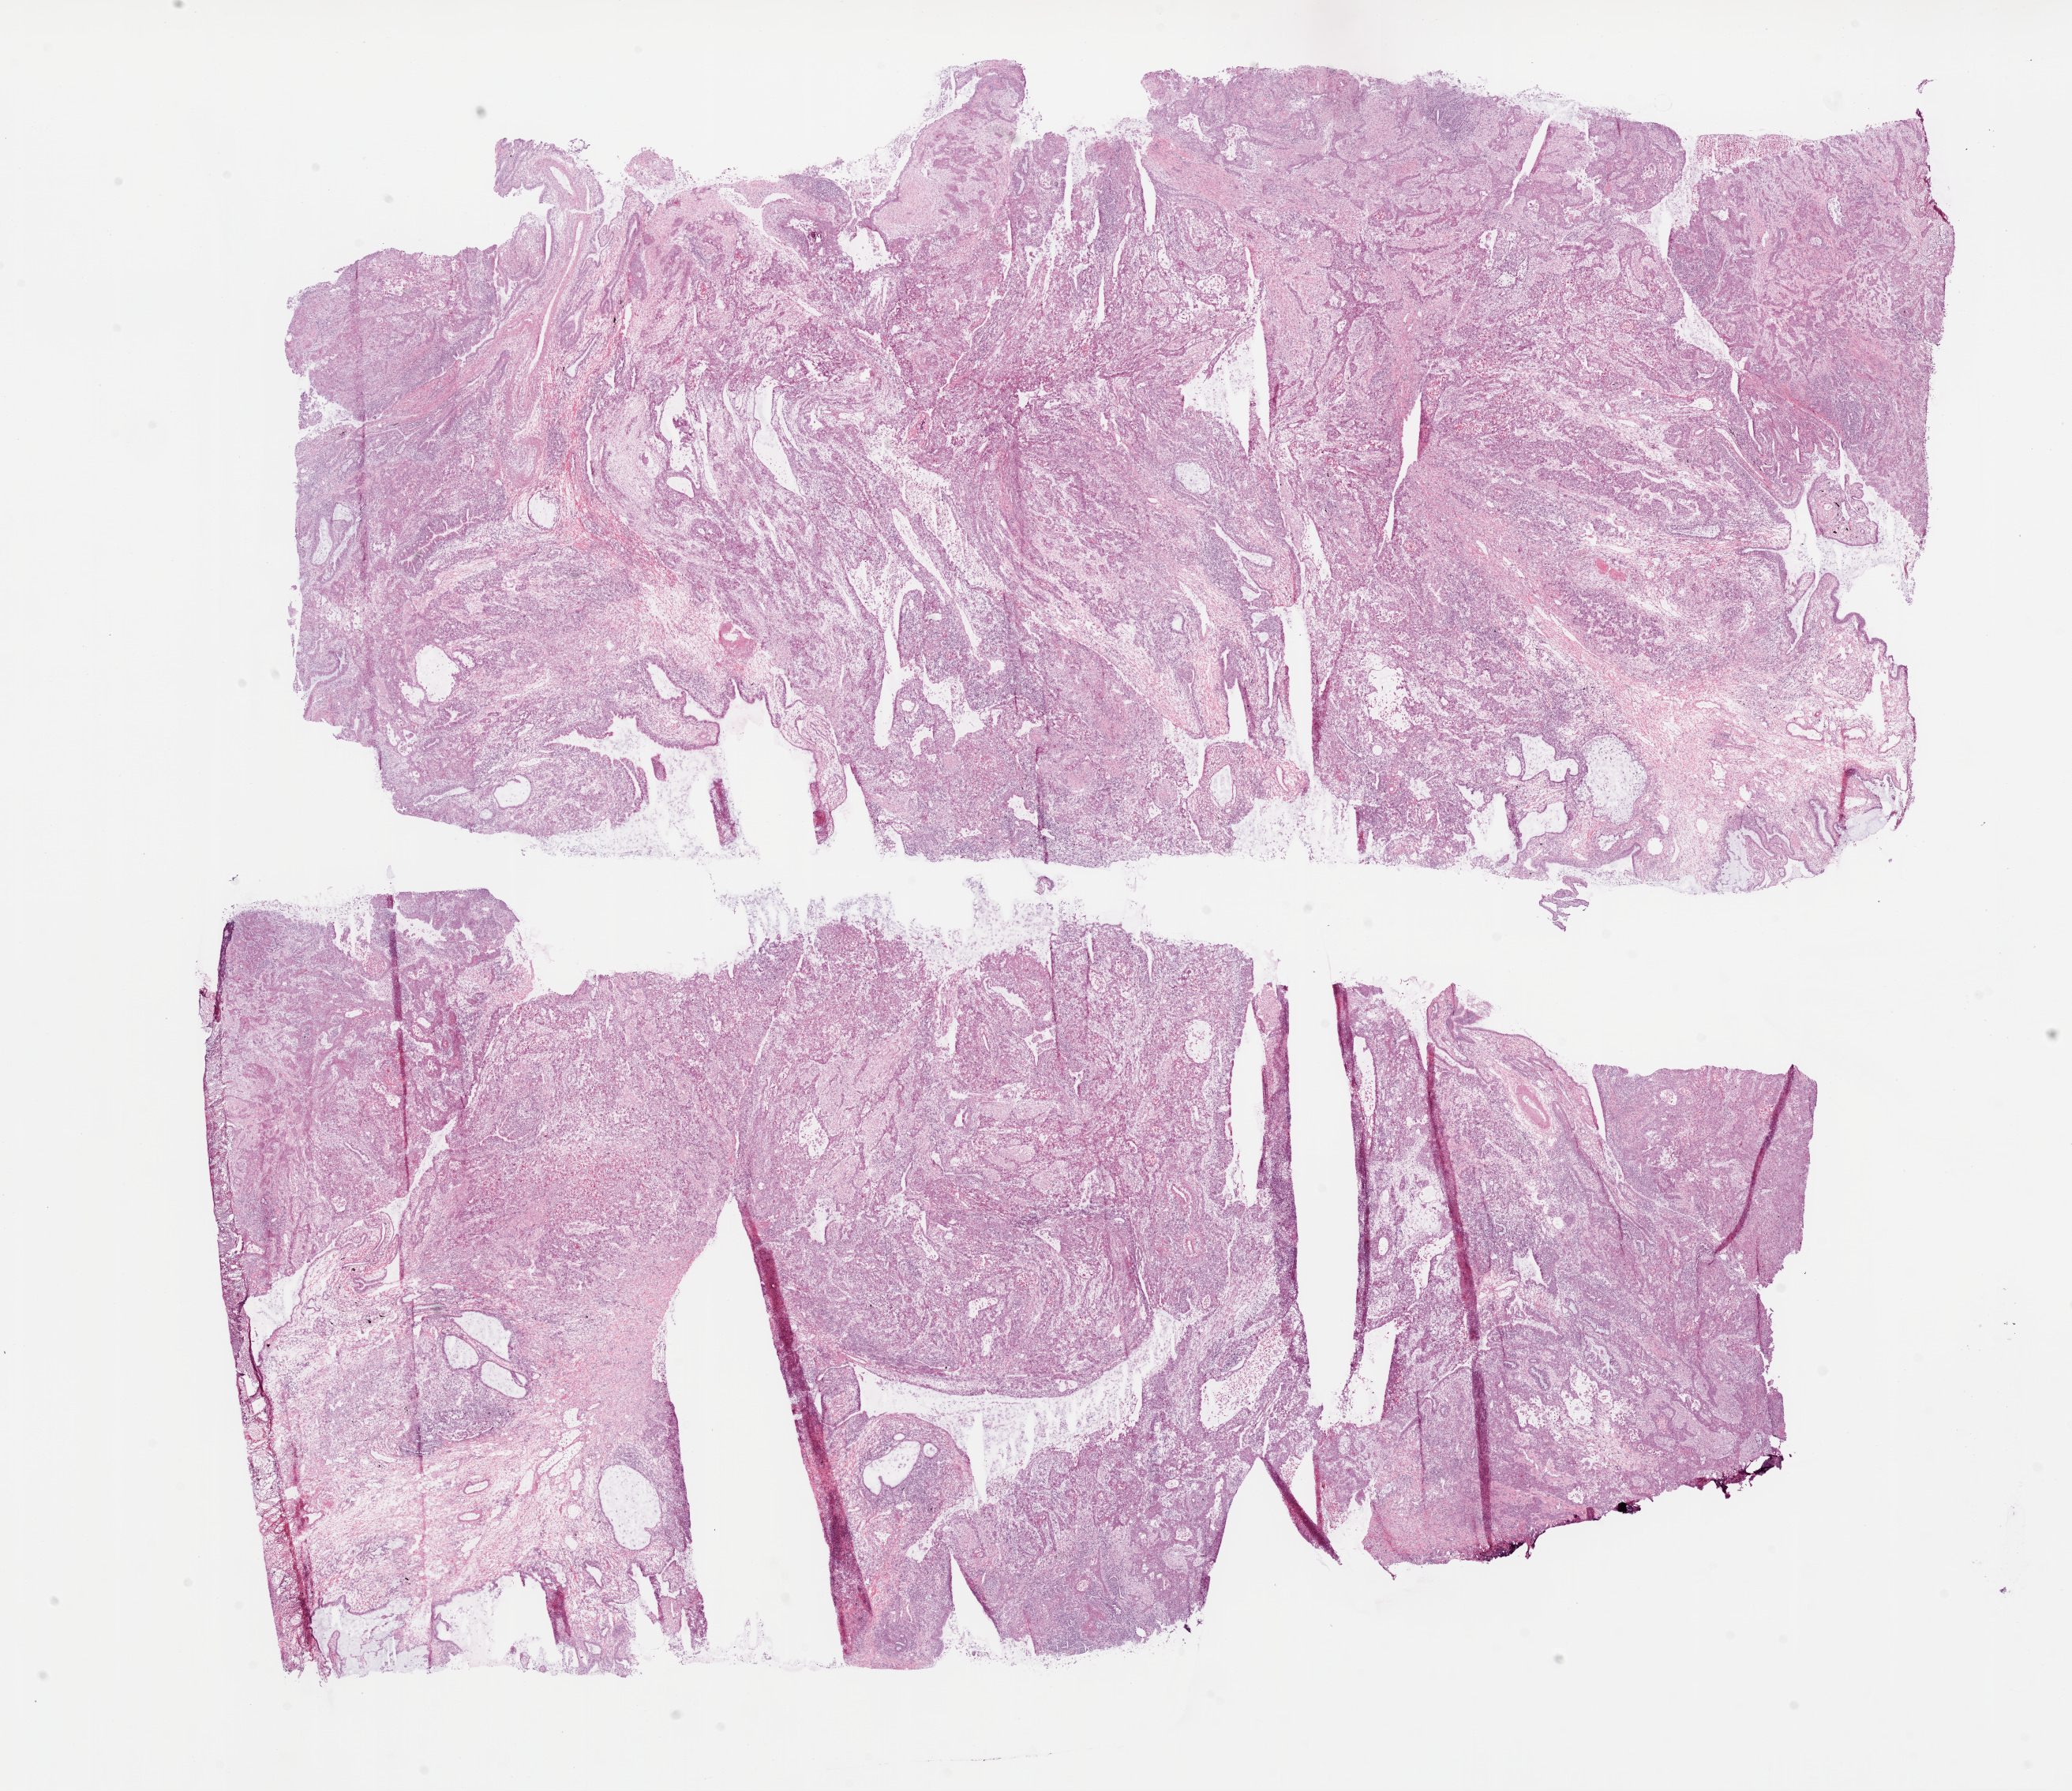
Digitized H&E-stained tissue section (whole slide) — shown as a low-resolution overview of the whole scanned area (about 21.1 x 18.2 mm, from a 20x scan). Frozen section. Lung, primary tumour sample. Male, age 75 years at initial diagnosis. Pathologist review of this section (percent, as recorded): tumour cells 62%, tumour nuclei 70%.
Histologic diagnosis: Squamous cell carcinoma, NOS (upper lobe, lung).